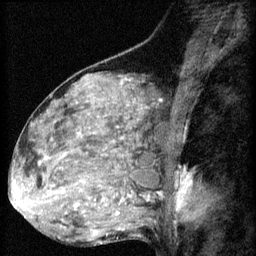
Breast MRI (dynamic contrast-enhanced), one sagittal slice. Position 35 of 60 along the scan axis. 3 images stored at this slice position (order not interpretable as contrast timing). 1.5 T. TE 4.2 ms, TR 8.2 ms. 256 × 256 image matrix, field of view 180 × 180 mm. Female patient, age 48 years.
Outlined on this slice (semi-automatically segmented with operator editing):
- analysis volume of interest (the breast-tissue region the enhancement analysis was run in; not a lesion): bounding box [x1, y1, x2, y2] px = [48, 160, 125, 217]
- tumour enhancement mask (voxels above the 70 % enhancement threshold inside the analysis volume of interest): [80, 180, 121, 203]